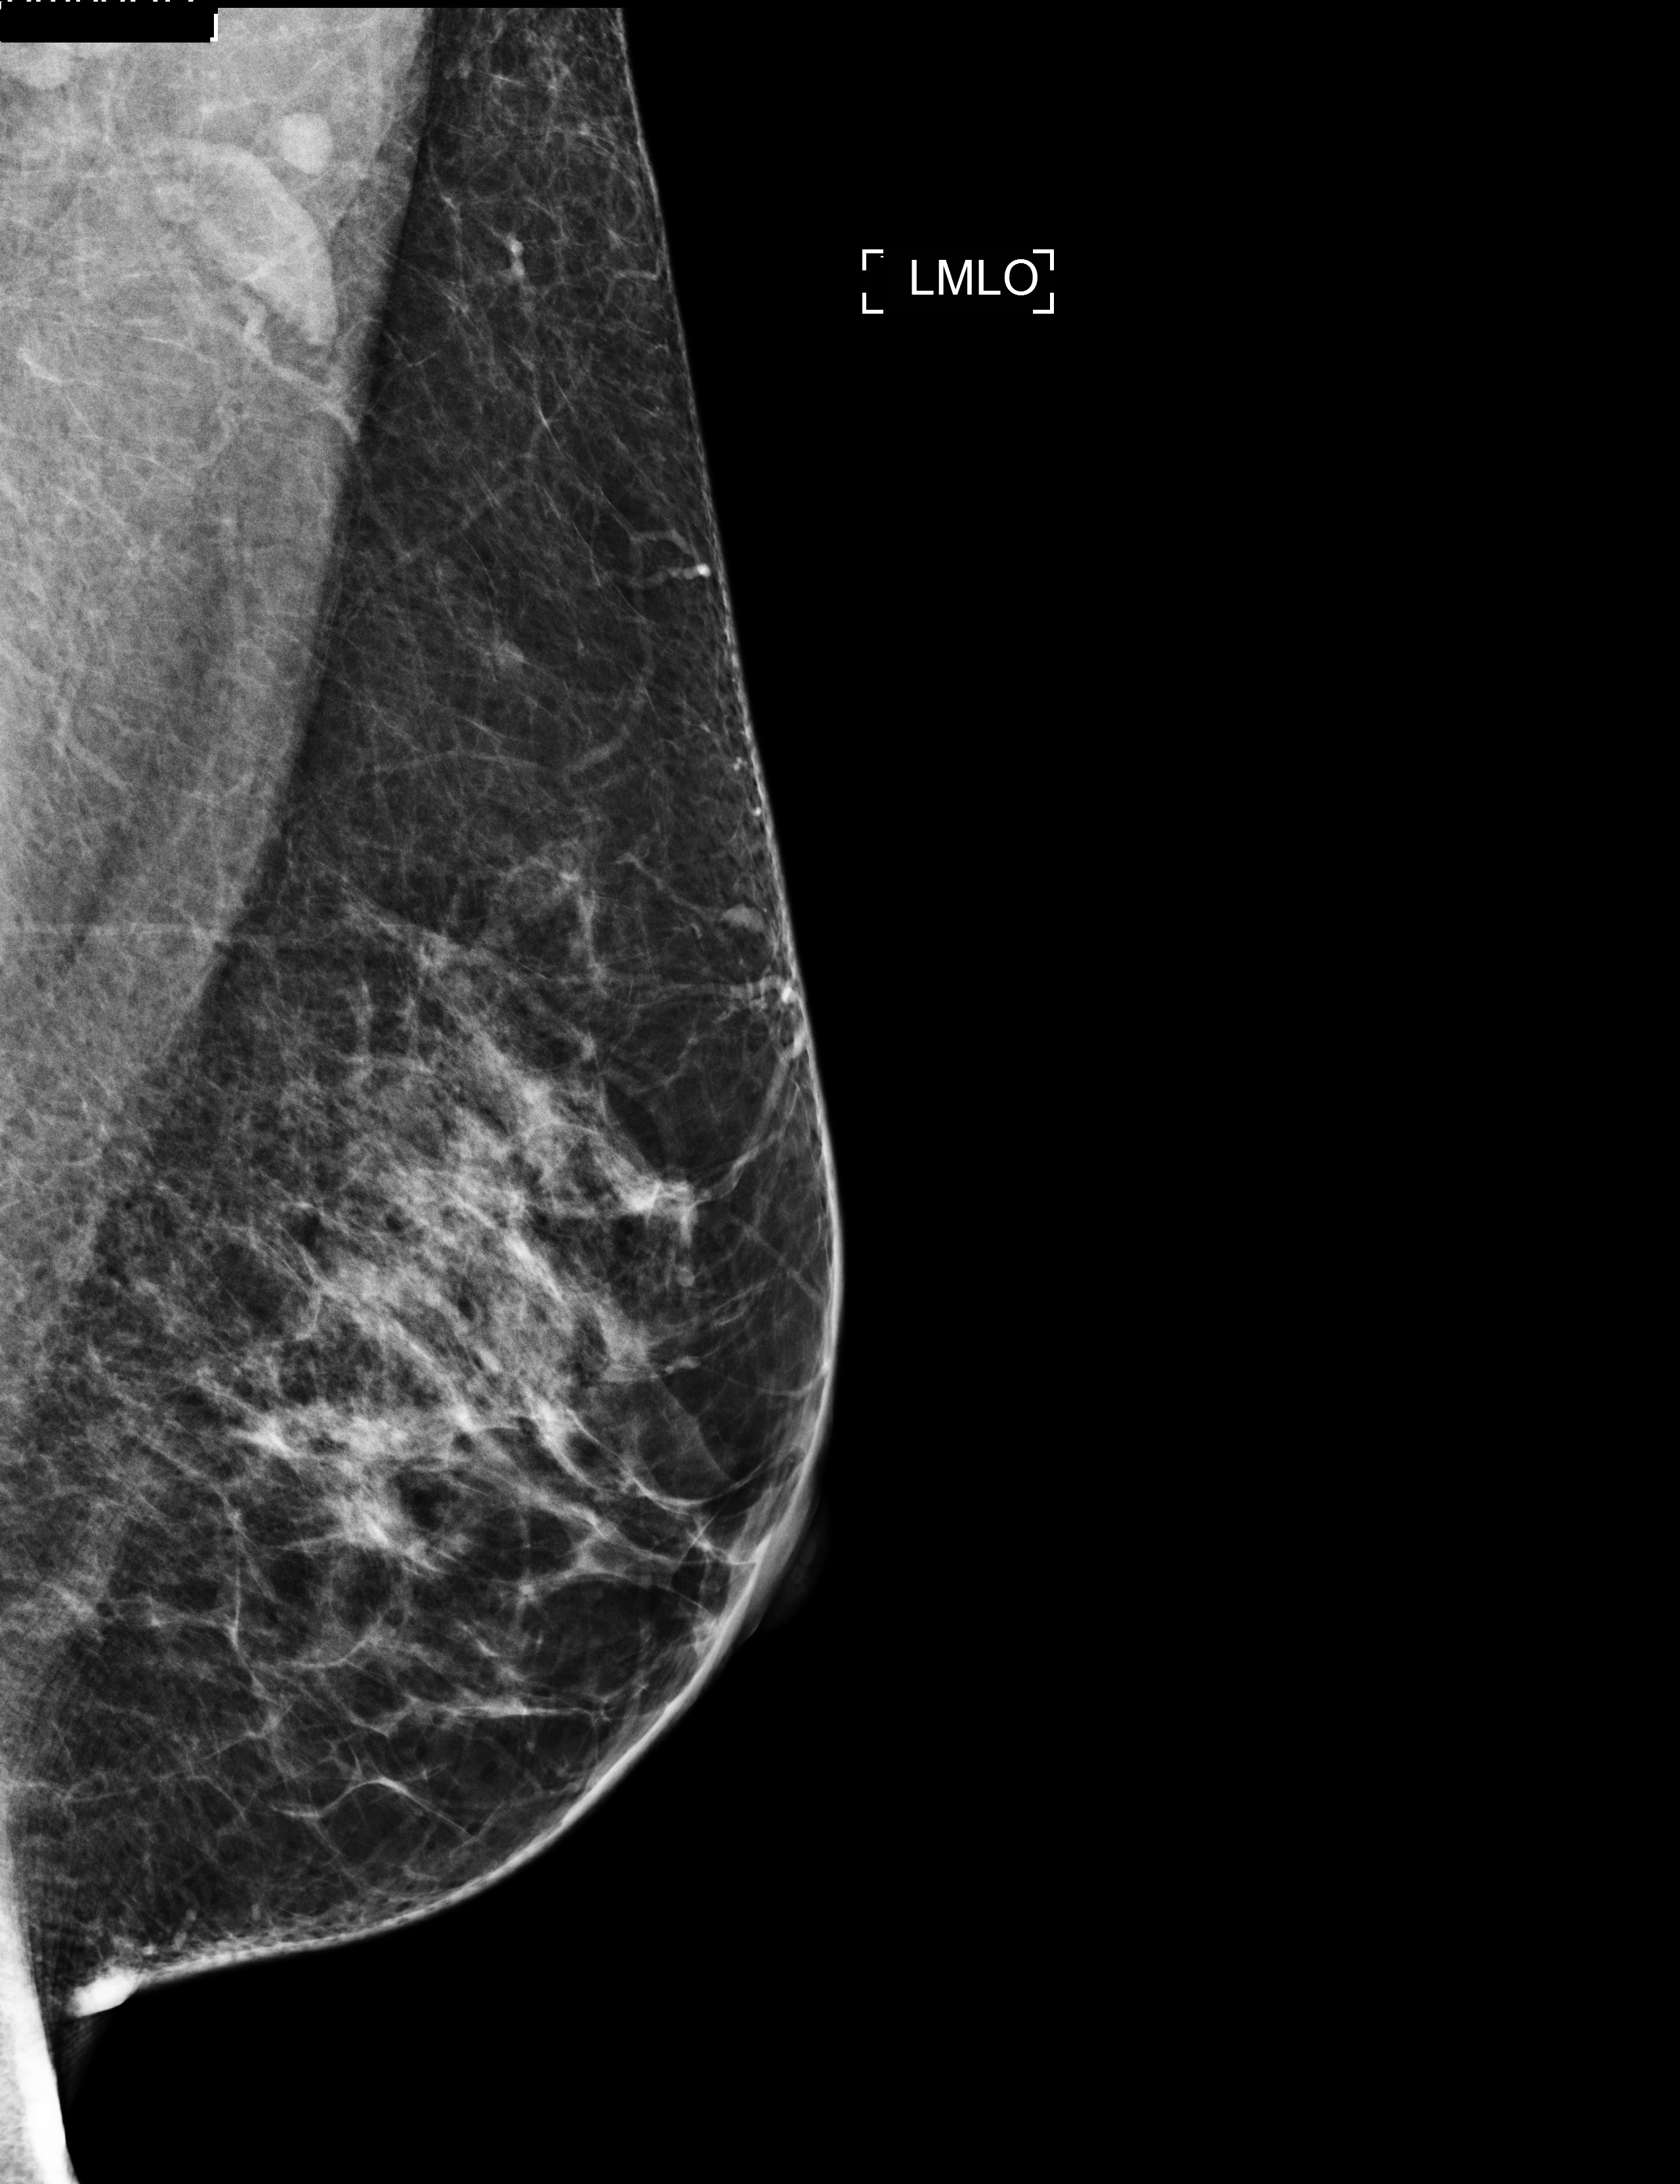
Full-field digital mammogram (FFDM); left breast; MLO view; screening examination; system: Selenia Dimensions. Patient: female, 44 years.
- BI-RADS breast density category at the screening exam (both breasts, scale 1–4): 3
- final BI-RADS category for the screening round (tomosynthesis exam, both breasts): category 1
- recall: no recall after this screen